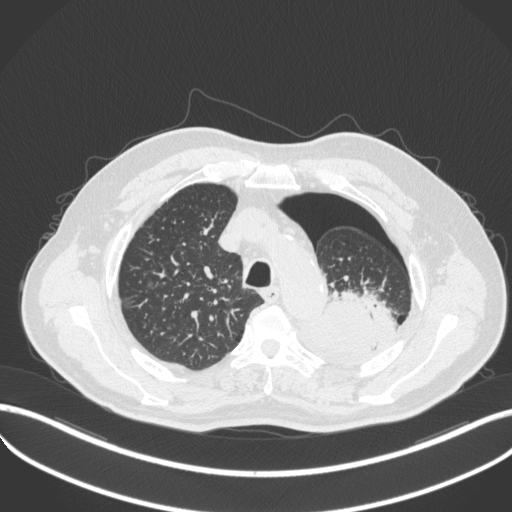
Chest CT, one axial slice. Slice 394 of 466 in the series (ordered by position). Lung window (W 1500 / L -600 HU). 1 mm slice thickness. 512 × 512 image matrix. Patient: male, 76 years. From the clinical record (not read from this slice): clinical TNM (as recorded): T3 N0 M1b.
Outlined on this slice (rectangle marked by the reading radiologist):
- lung tumour (recorded histology: adenocarcinoma): bounding box [x1, y1, x2, y2] px = [317, 296, 380, 362]